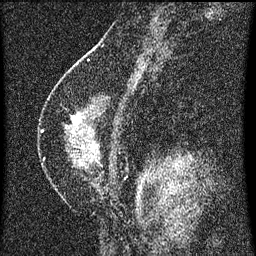
Breast MRI (dynamic contrast-enhanced), one sagittal slice. Slice 40 of 60 in the series (ordered by position). Dynamic contrast-enhanced series, image 2 of 3 at this slice position (ordered by acquisition). 1.5 T. TE 4.2 ms, TR 8 ms. 256 × 256 image matrix, field of view 180 × 180 mm. Female patient, age 47 years.
Annotated regions visible in this slice (semi-automatically segmented with operator editing):
- analysis volume of interest (the breast-tissue region the enhancement analysis was run in; not a lesion): box from (x=42, y=92) to (x=131, y=197) px
- tumour enhancement mask (voxels above the 70 % enhancement threshold inside the analysis volume of interest): (x=72, y=114)–(x=80, y=123)